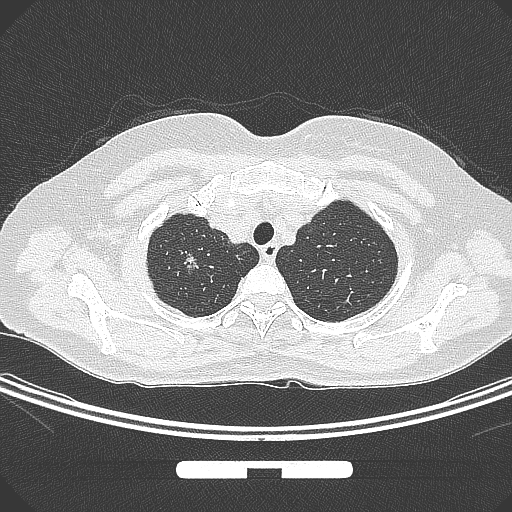
Chest CT, one axial slice. Slice 255 of 295 in the series (ordered by position). Lung window (W 1500 / L -600 HU). 512 × 512 image matrix. Patient: female, 58 years. Case-level facts recorded for this patient, not image findings: clinical TNM (as recorded): T1b N0 M0; histopathological grade: G2-3.
Structures marked on this image (bounding box drawn by a radiologist):
- lung tumour (recorded histology: adenocarcinoma): bounding box <178,240,212,284> (left, top, right, bottom; pixels)